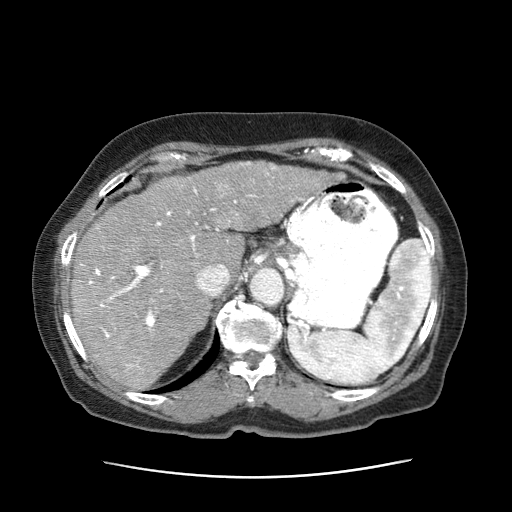
Contrast-enhanced abdominal CT (liver protocol), one axial slice; slice 47 of 63 in the series (ordered by position); reconstruction kernel STANDARD; 120 kVp; intravenous contrast given; soft-tissue window (W 400 / L 40 HU); 2.5 mm slice thickness; 512 × 512 image matrix. Female patient, age 79 years. Case-level facts recorded for this patient, not image findings: diagnosis: hepatocellular carcinoma (patient treated with transarterial chemoembolisation; whether this scan precedes or follows treatment is not stated here); TNM stage (as recorded): Stage-II; Child-Pugh class: B; tumour differentiation: well differentiated; tumour nodularity: multinodular.
Annotated regions visible in this slice (semi-automatic segmentation, software-assisted and operator-edited):
- abdominal aorta: bounding box <249,270,286,307> (left, top, right, bottom; pixels)
- liver parenchyma outside the tumour (the mass and vessels are separate outlines, so this box may not span the whole liver): <72,177,247,392>
- mass: <183,162,342,229>
- liver vessels: <86,179,298,359>